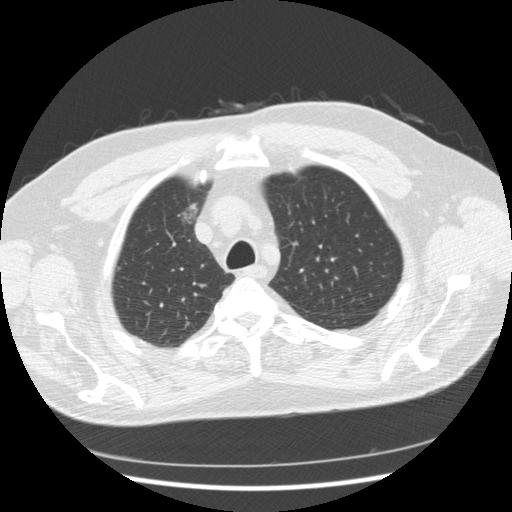
Low-dose screening chest CT, axial slice. Second annual screen. Lung window (W 1500 / L -600 HU). Standard (soft-tissue) reconstruction kernel (STANDARD). Slice 46 of 267 in the series. 512 × 512 image matrix, field of view 360 × 360 mm. Male participant, aged 66 years at enrolment. Former smoker at enrolment.
• Expert reader's lesion annotation, bounding box [x1, y1, x2, y2] px = [158, 197, 212, 239].
• No non-calcified nodule or mass ≥4 mm was recorded by the screening reader at this exam.
• Official screen result: positive, other.
• Participant outcome: lung cancer diagnosed 603 days after this screen (after the third annual screen) — bronchiolo-alveolar adenocarcinoma, NOS, right upper lobe, moderately differentiated (G2), stage IA (AJCC 6th edition), 12 mm at pathology.